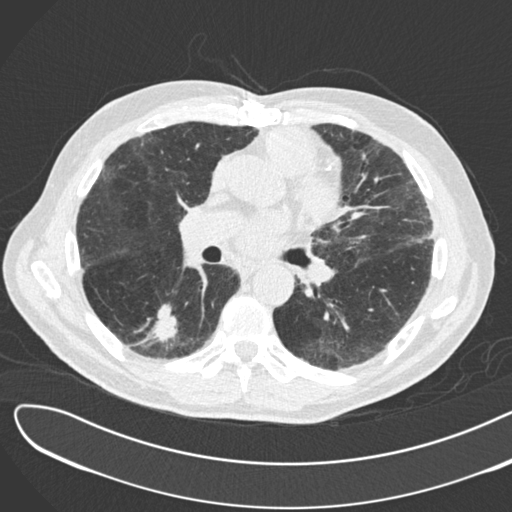
Low-dose screening chest CT, one axial slice; slice 91 of 183 in the series (ordered by position); lung window (W 1500 / L -600 HU); 2 mm slice thickness; 512 × 512 image matrix, field of view 370 × 370 mm.
Structures marked on this image (expert manual segmentation):
- lesion 1 (tumor, lower lobe of right lung): box from (x=153, y=304) to (x=178, y=343) px